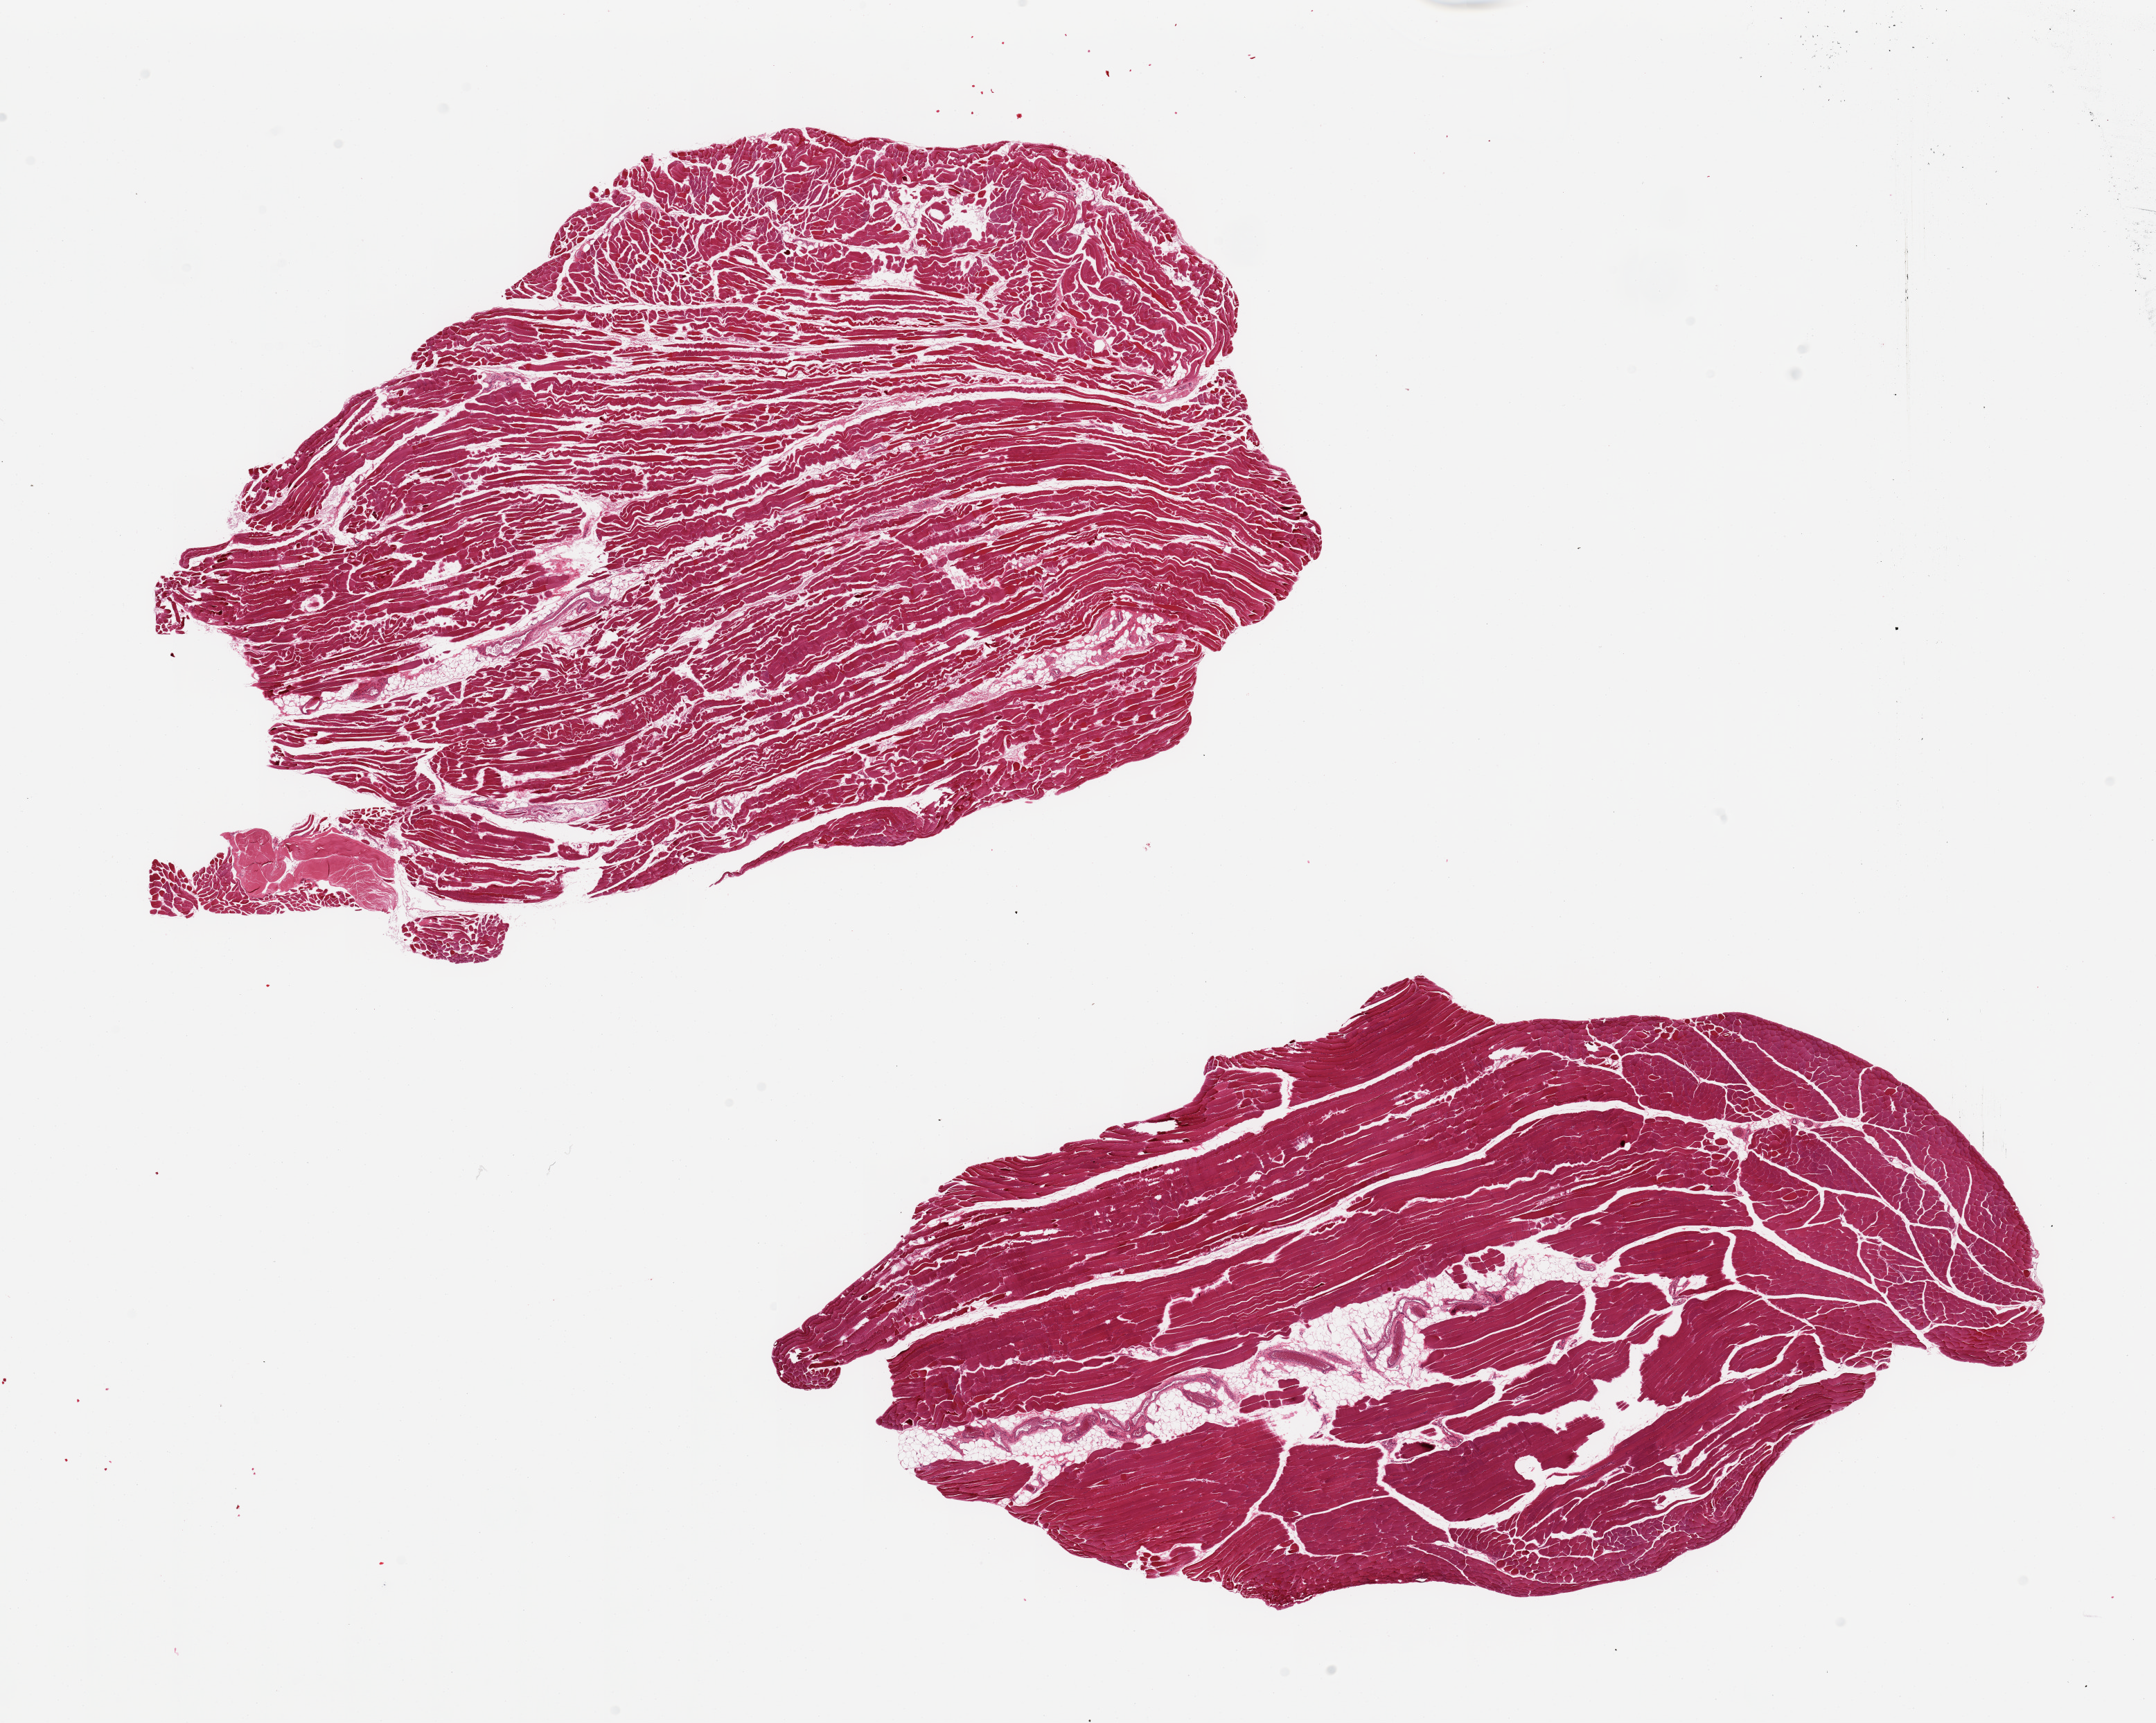
Whole-slide image, hematoxylin and eosin (H&E) stain, brightfield — whole scanned area (about 24.6 x 19.7 mm, slide scanned at 20x) shown as a low-resolution overview; PAXgene-fixed paraffin-embedded (PFPE) section; target tissue: skeletal muscle; donor tissue sample. Donor sex: male.
* review note (as recorded): 2 pieces; moderate atrophy in 1; 10% internal fat